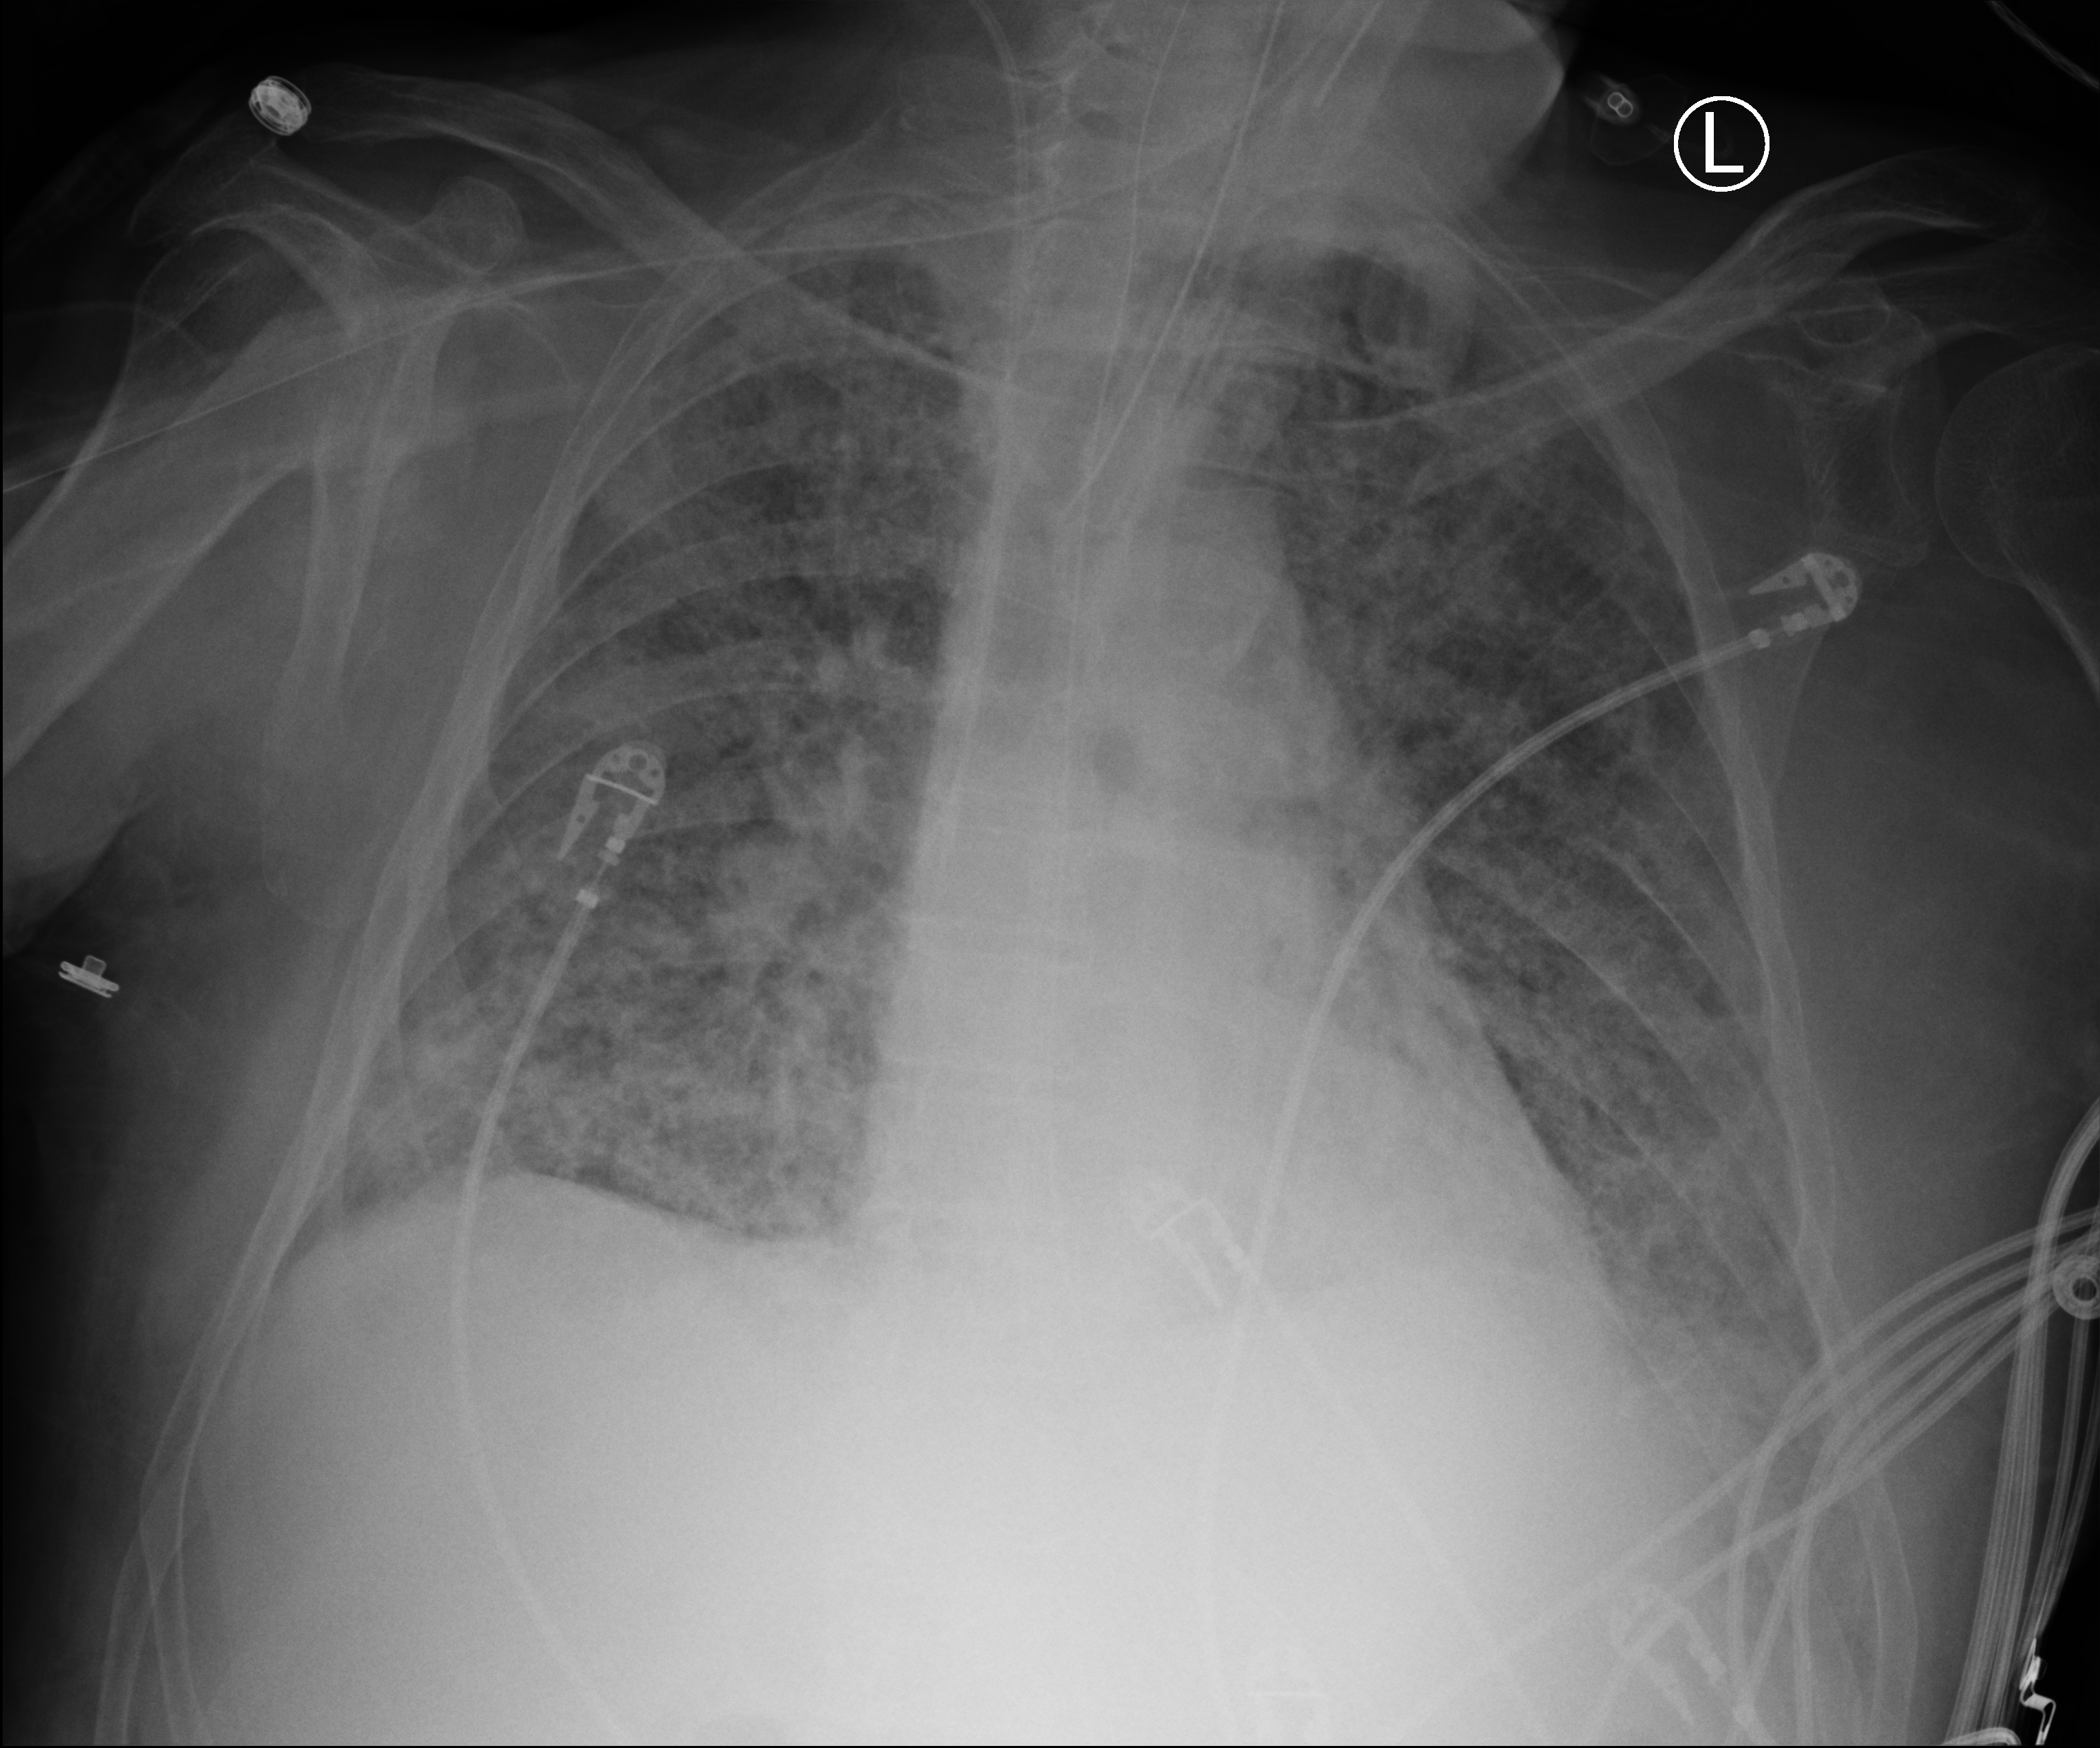
Chest X-ray (portable), anteroposterior (AP) projection. Patient hospitalised with COVID-19; male, aged 60–74 years.
Hospital-stay facts (about this admission, not read from this image; timing relative to this image not recorded):
- mechanically ventilated during this hospital stay: yes
- admitted to intensive care during this hospital stay: yes